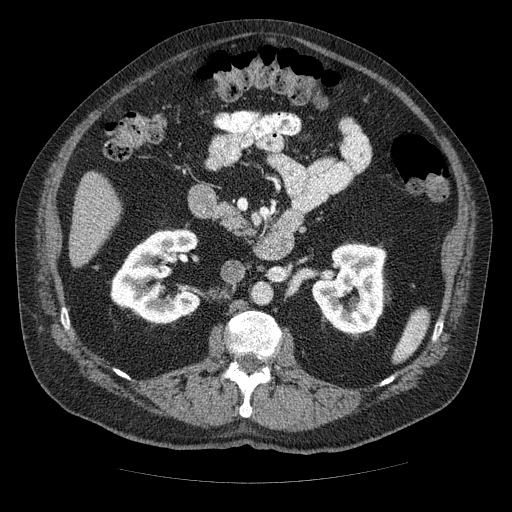
Contrast-enhanced abdominal CT (liver protocol), one axial slice; slice 12 of 85 in the series (ordered by position); 120 kVp; soft-tissue window (W 400 / L 40 HU); 512 × 512 image matrix, field of view 420 × 420 mm. From the clinical record (not read from this slice): diagnosis: hepatocellular carcinoma (patient treated with transarterial chemoembolisation; whether this scan precedes or follows treatment is not stated here); TNM stage (as recorded): Stage-IIIA; Child-Pugh class: A.
Structures marked on this image (semi-automatic segmentation, software-assisted and operator-edited):
- liver parenchyma outside the tumour (the mass and vessels are separate outlines, so this box may not span the whole liver): bounding box (x1, y1, x2, y2) in pixels: (68, 172, 120, 266)